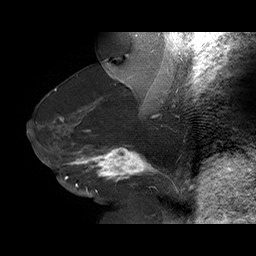
Breast MRI (dynamic contrast-enhanced), one sagittal slice; slice 38 of 75 in the series (ordered by position); dynamic contrast-enhanced series, time point 2 of 6 at this slice position (early post-contrast); 1.5 T; TE 4.5 ms, TR 32.4 ms; 3 mm slice thickness; 256 × 256 image matrix, field of view 180 × 180 mm. Female patient. Case-level facts recorded for this patient, not image findings: setting: breast cancer imaged before/during neoadjuvant chemotherapy; receptor status: HR-positive, HER2-negative.
Structures marked on this image (semi-automatic segmentation, software-assisted and operator-edited):
- analysis volume of interest (the breast-tissue region the enhancement analysis was run in; not a lesion): box from (x=58, y=134) to (x=166, y=191) px
- tumour enhancement mask (voxels above the 100 % enhancement threshold inside the analysis volume of interest): (x=65, y=147)–(x=153, y=186)